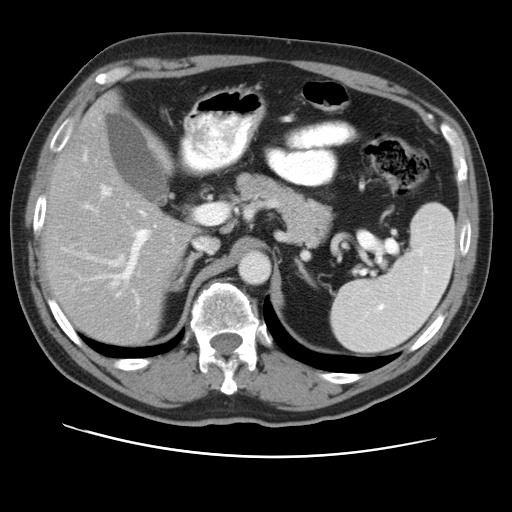
Contrast-enhanced abdominal CT, one axial slice. Reconstruction kernel STANDARD. 120 kVp. Intravenous contrast given. Soft-tissue window (W 400 / L 40 HU). 5 mm slice thickness. 512 × 512 image matrix. Male patient, age 59 years. From the clinical record (not read from this slice): diagnosis: colorectal cancer liver metastases, imaged before liver resection; multiple liver metastases: yes; largest metastasis: 6.3 cm; disease in both lobes: yes.
Structures marked on this image (outlined manually by an expert reader):
- hepatic veins: bounding box (x1, y1, x2, y2) in pixels: (102, 186, 215, 253)
- liver: (46, 101, 192, 343)
- planned liver remnant (the part of the liver to remain after resection): (47, 102, 192, 343)
- portal vein (with intrahepatic branches): (82, 149, 220, 296)